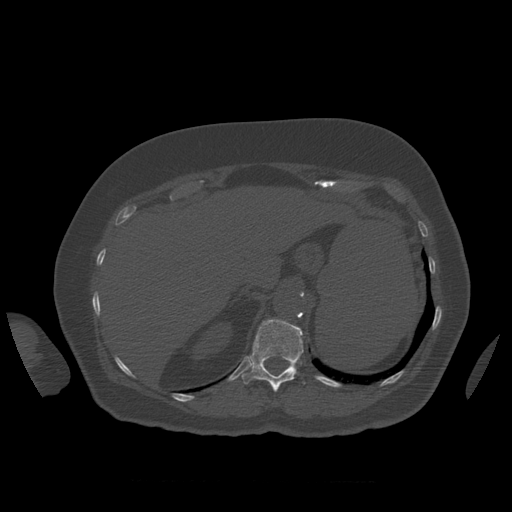
CT including the spine, one axial slice. 120 kVp. Bone window (W 1800 / L 400 HU). 1.25 mm slice thickness. 512 × 512 image matrix. Patient age 81 years. From the clinical record (not read from this slice): primary cancer: renal.
Structures marked on this image (semi-automatically segmented with operator editing):
- T12 vertebra: box from (x=242, y=319) to (x=305, y=392) px